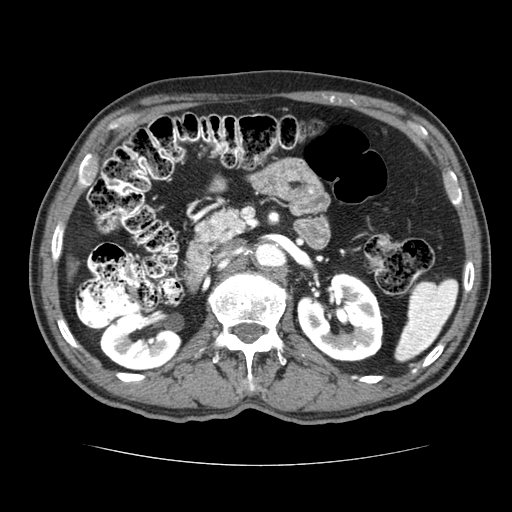
Contrast-enhanced abdominal CT (liver protocol), one axial slice. Reconstruction kernel STANDARD. 120 kVp. Soft-tissue window (W 400 / L 40 HU). 2.5 mm slice thickness. 512 × 512 image matrix, field of view 360 × 360 mm. From the clinical record (not read from this slice): diagnosis: hepatocellular carcinoma (patient treated with transarterial chemoembolisation; whether this scan precedes or follows treatment is not stated here); TNM stage (as recorded): Stage-I.
Annotated regions visible in this slice (semi-automatic segmentation, software-assisted and operator-edited):
- liver parenchyma outside the tumour (the mass and vessels are separate outlines, so this box may not span the whole liver): box from (x=66, y=264) to (x=75, y=281) px